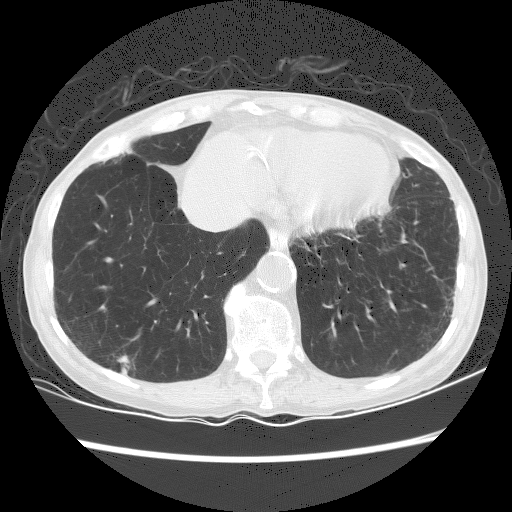
Axial slice from a low-dose chest CT screening exam. Baseline screening round. Lung window (W 1500 / L -600 HU). 2.5 mm slice thickness. 120 kVp. Slice 103 of 156 in the series. 512 × 512 image matrix, field of view 320 × 320 mm. Female participant, aged 70 years at enrolment.
Expert-annotated lung lesion, bounding box <98,343,153,385> (left, top, right, bottom; pixels). The screening reader recorded 2 non-calcified nodules or masses ≥4 mm on this exam; which of them this box marks is not recorded. Official screen result: positive, change unspecified: nodule(s) >= 4 mm or enlarging nodule(s), mass(es), or other non-specific abnormalities suspicious for lung cancer.